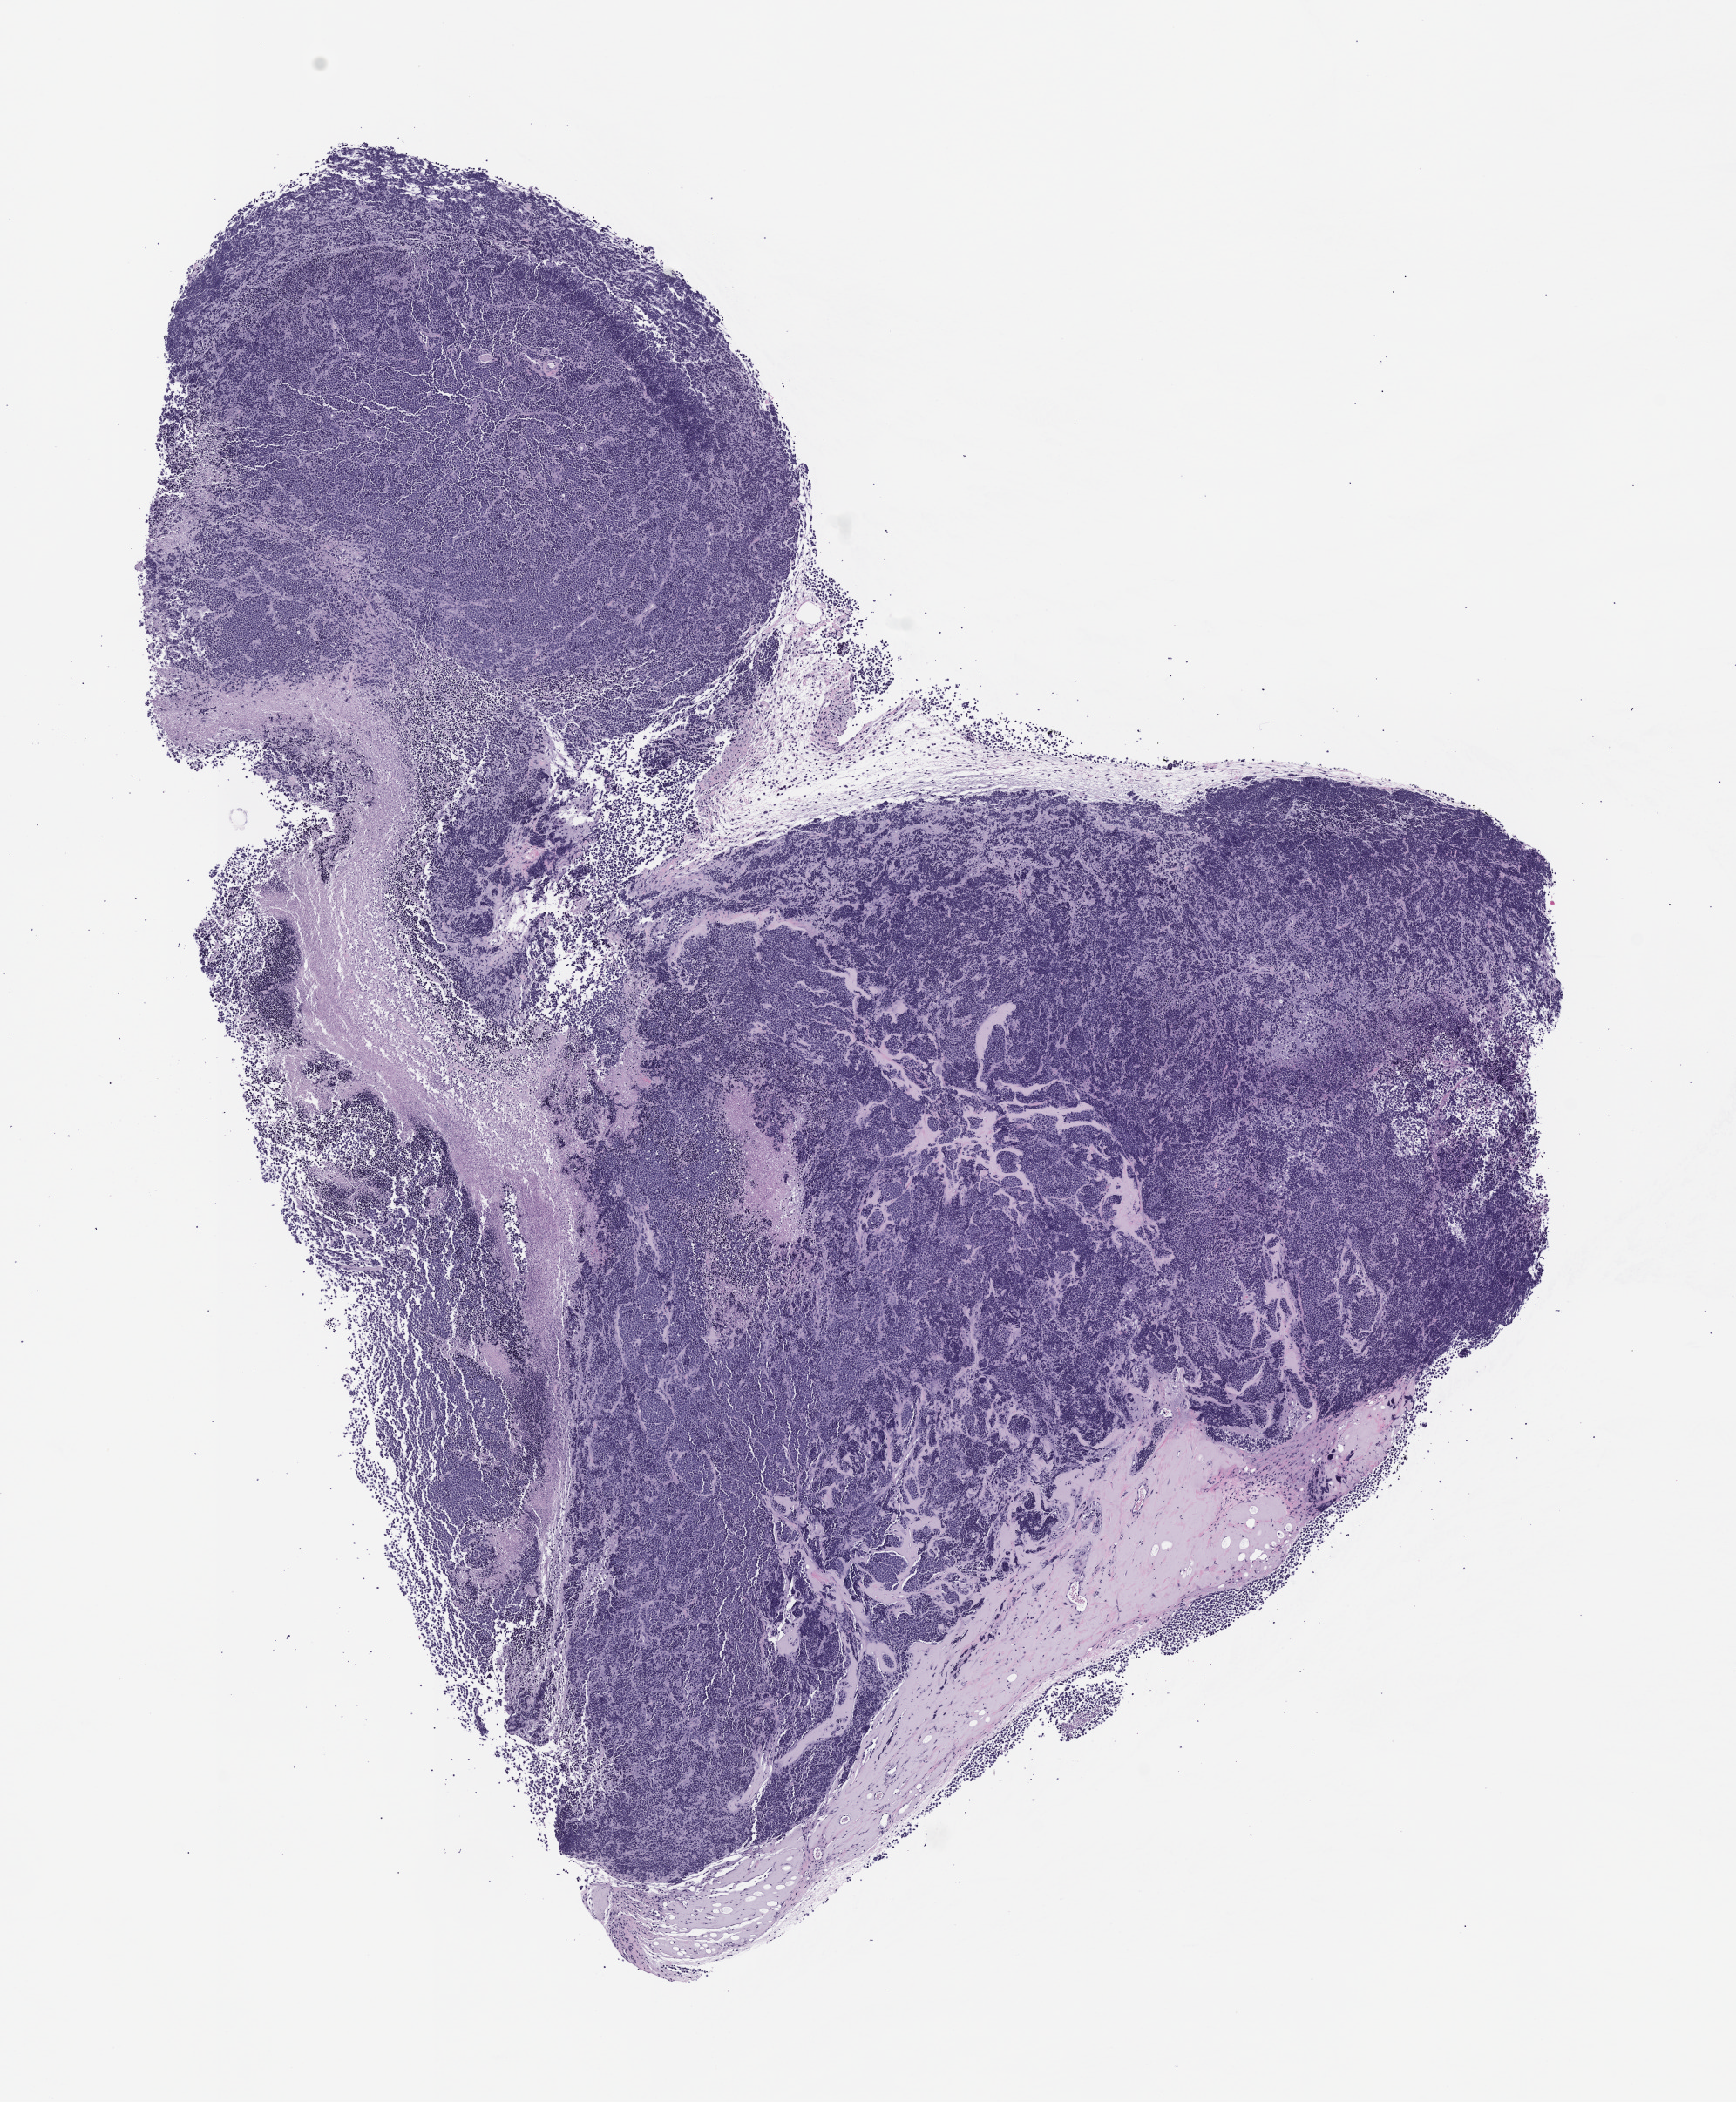
Whole-slide image, H&E: patient-derived xenograft (human tumor grown in a mouse), passage 0 — whole scanned area (about 8.0 x 9.7 mm) shown as a low-resolution overview. Formalin-fixed paraffin-embedded section. Tumor site category: lung.
Originating patient diagnosis: Lung Small Cell Carcinoma.